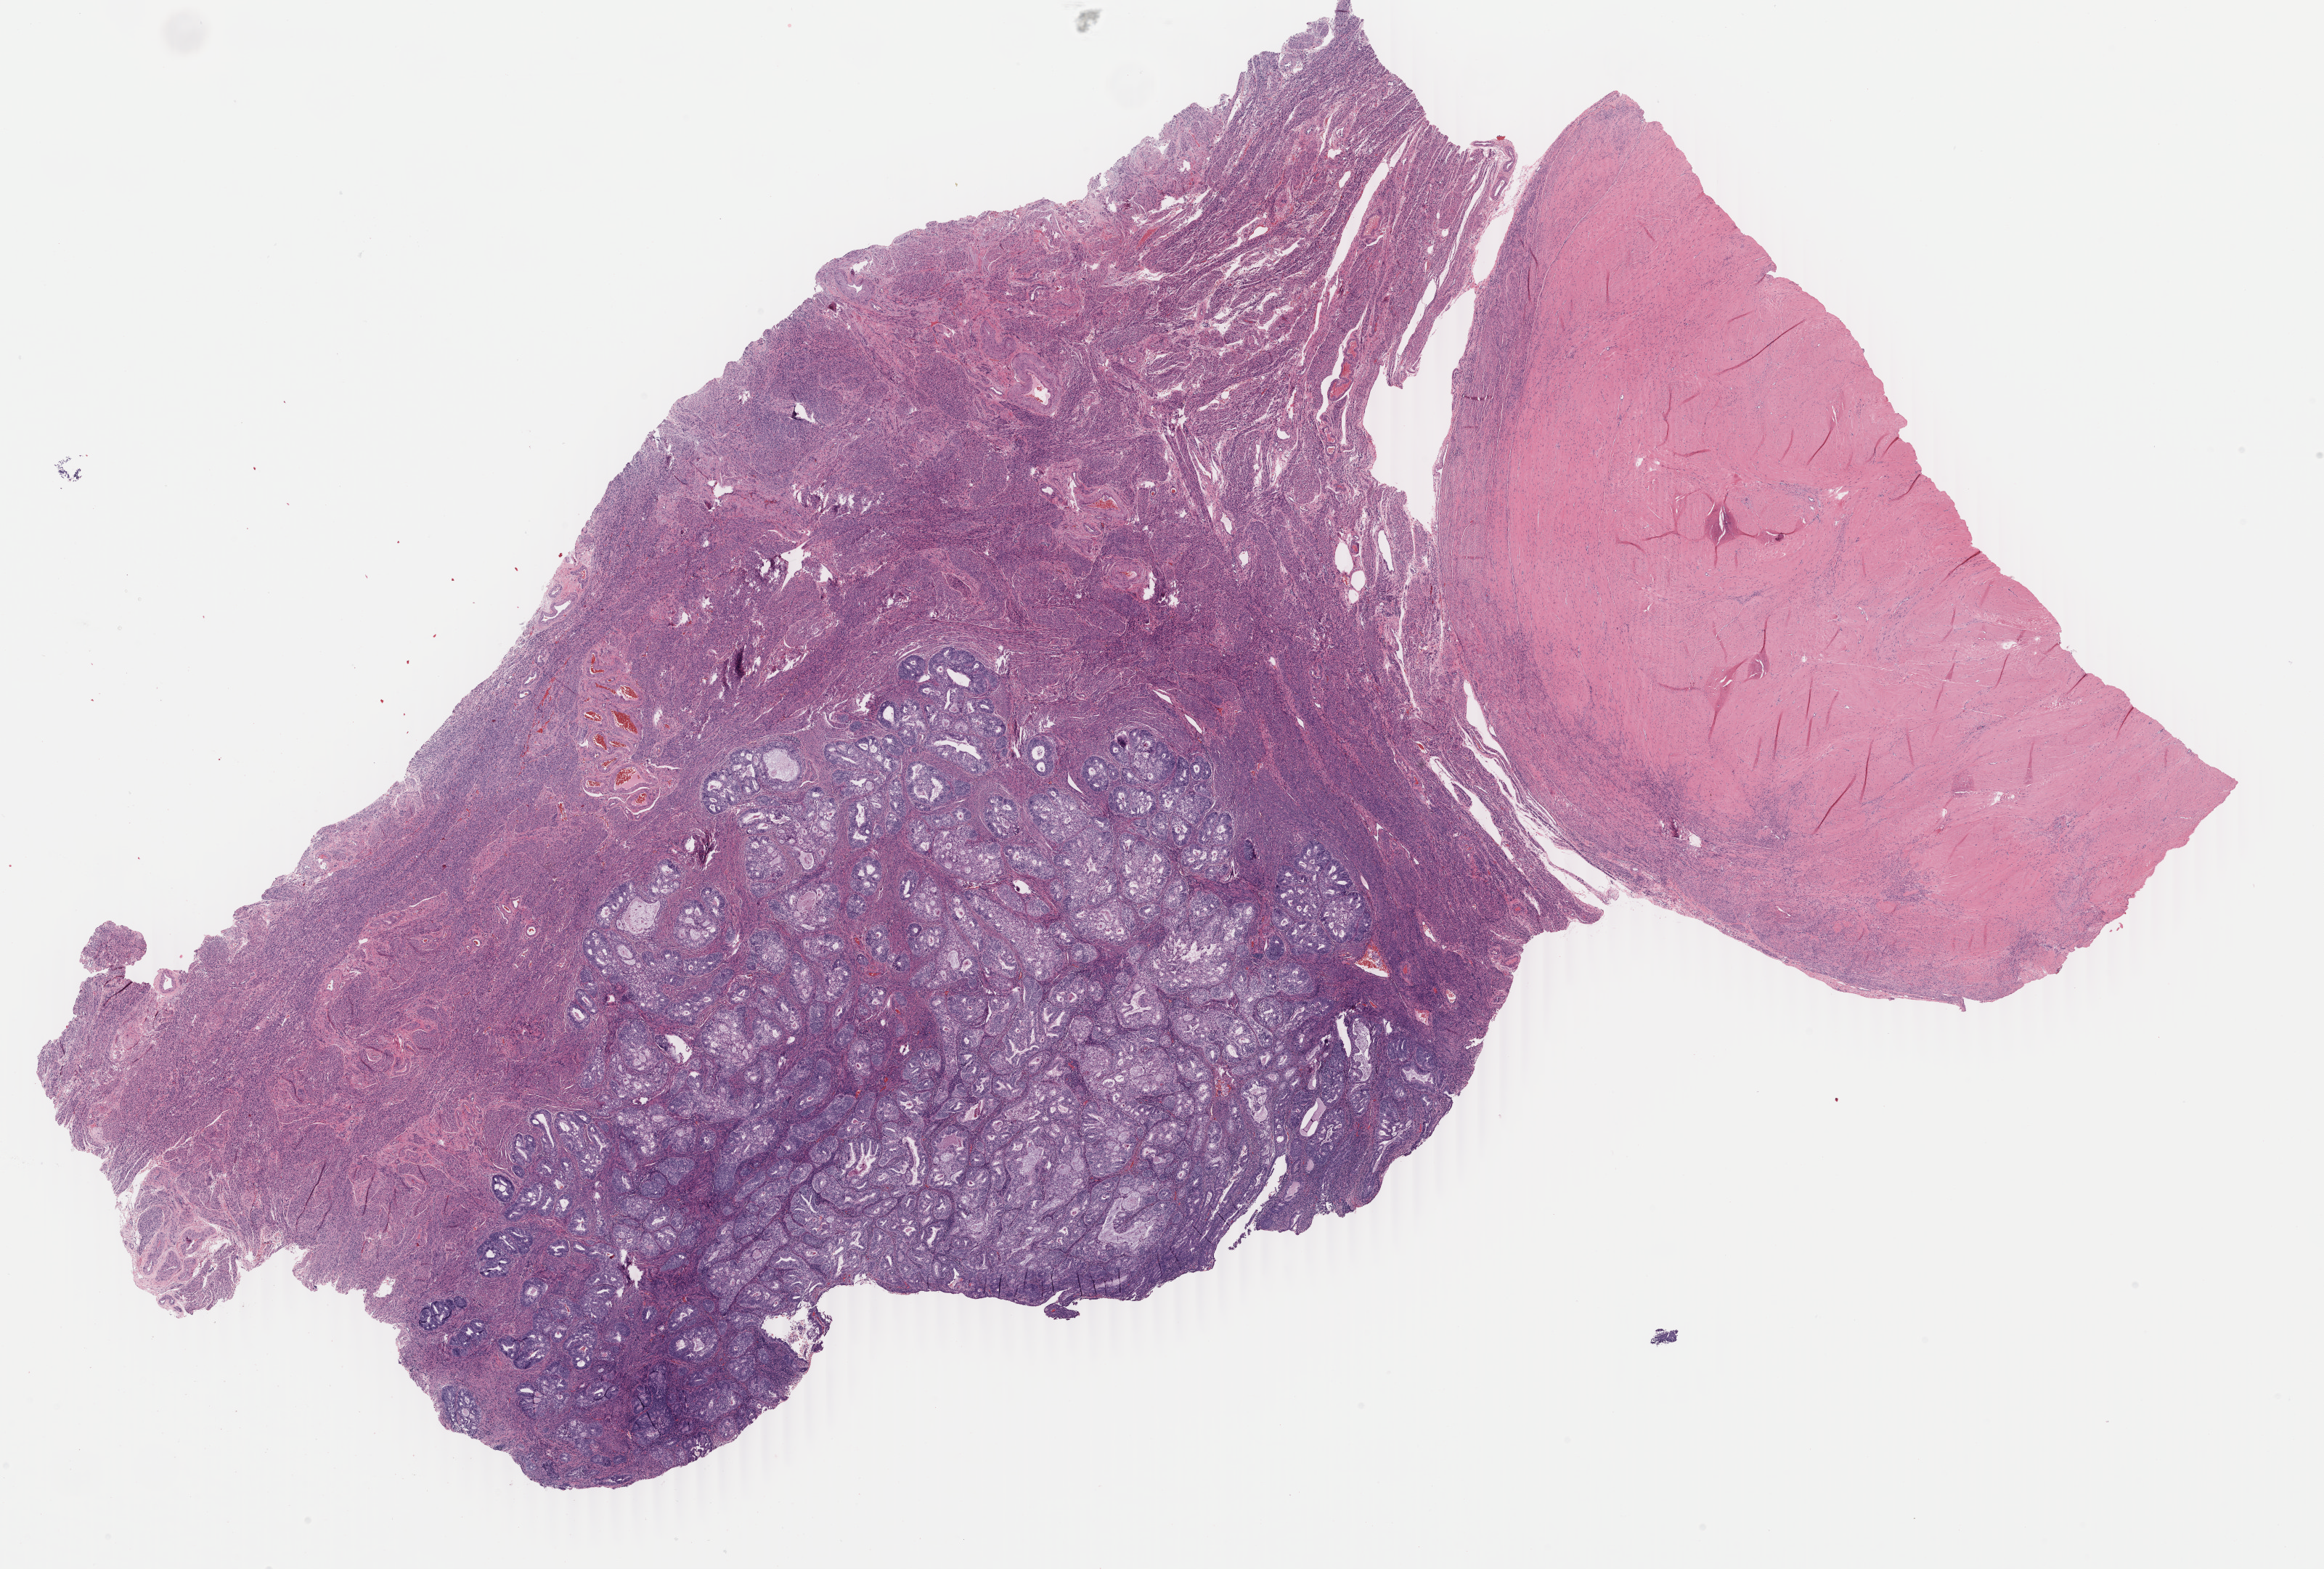
Hematoxylin and eosin (H&E) stained whole-slide image — whole scanned area (about 25.5 x 17.2 mm, from a 40x scan) shown as a low-resolution overview. Formalin-fixed paraffin-embedded (FFPE) diagnostic section. Sample: primary tumour, uterus. Female, age 74 years at initial diagnosis.
Diagnosis: Endometrioid adenocarcinoma, NOS (endometrium).